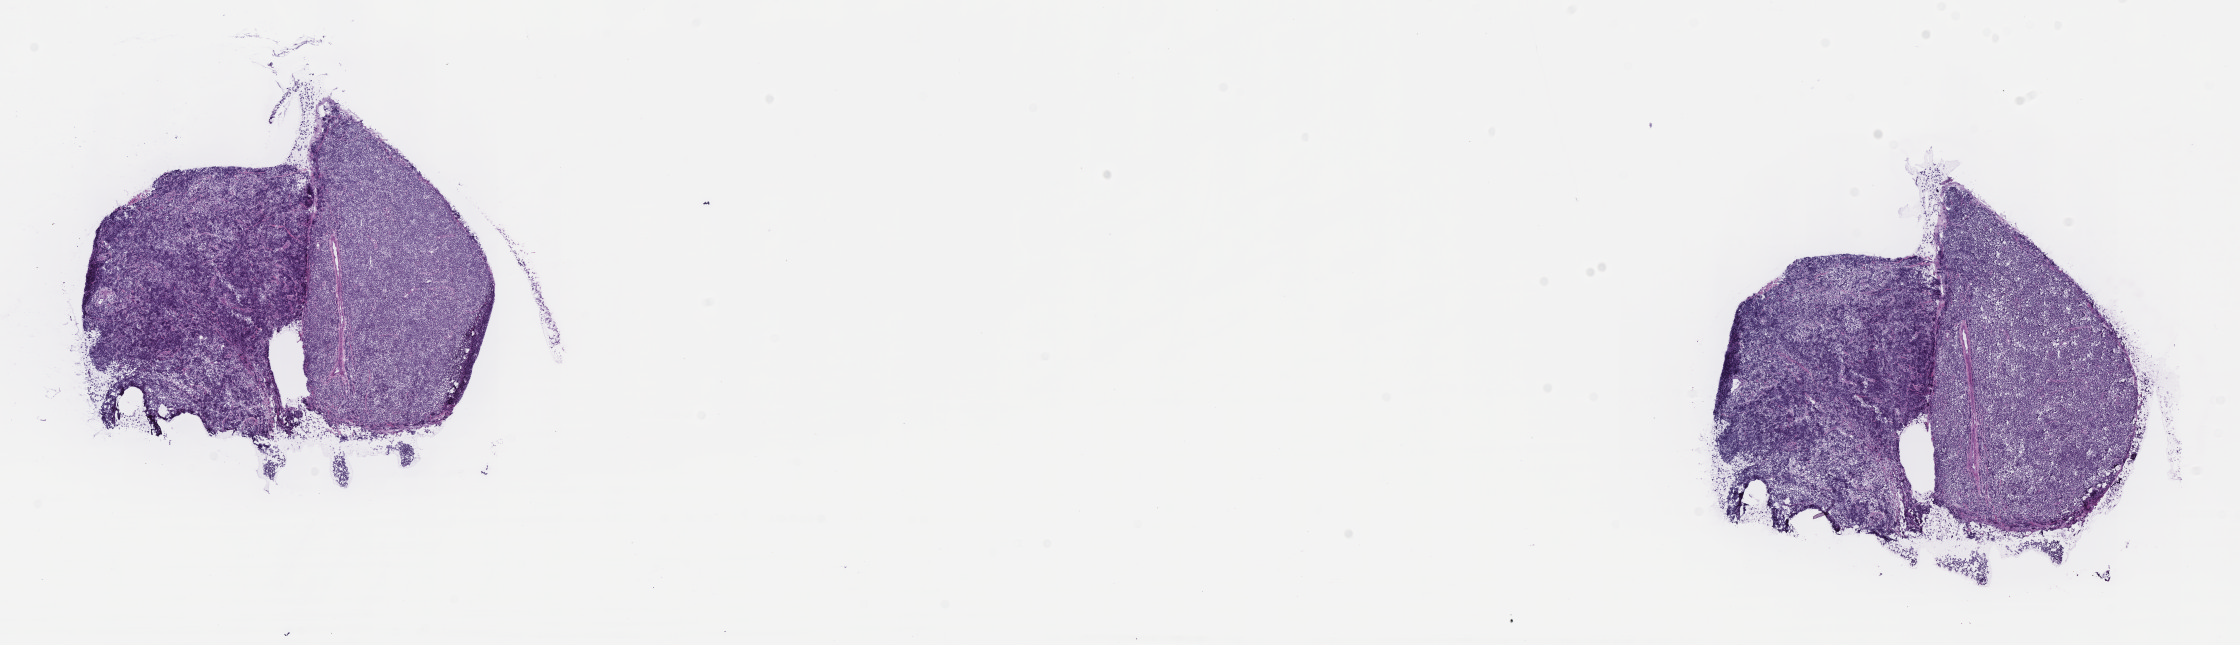
Haematoxylin and eosin whole-slide image — low-resolution overview of the scanned area, about 18.1 x 5.2 mm. Frozen section. Specimen: primary tumor. Site: cranium. Male patient; age at initial diagnosis 5 years. Slide review estimates, as recorded: tumor cells 90%, tumor nuclei 95%, stromal cells 5%, necrosis 5%, normal cells 0%. Inflammatory infiltration, as recorded: lymphocyte infiltration 70%, monocyte infiltration 15%, neutrophil infiltration 0%.
Diagnosis: Burkitt lymphoma, NOS.